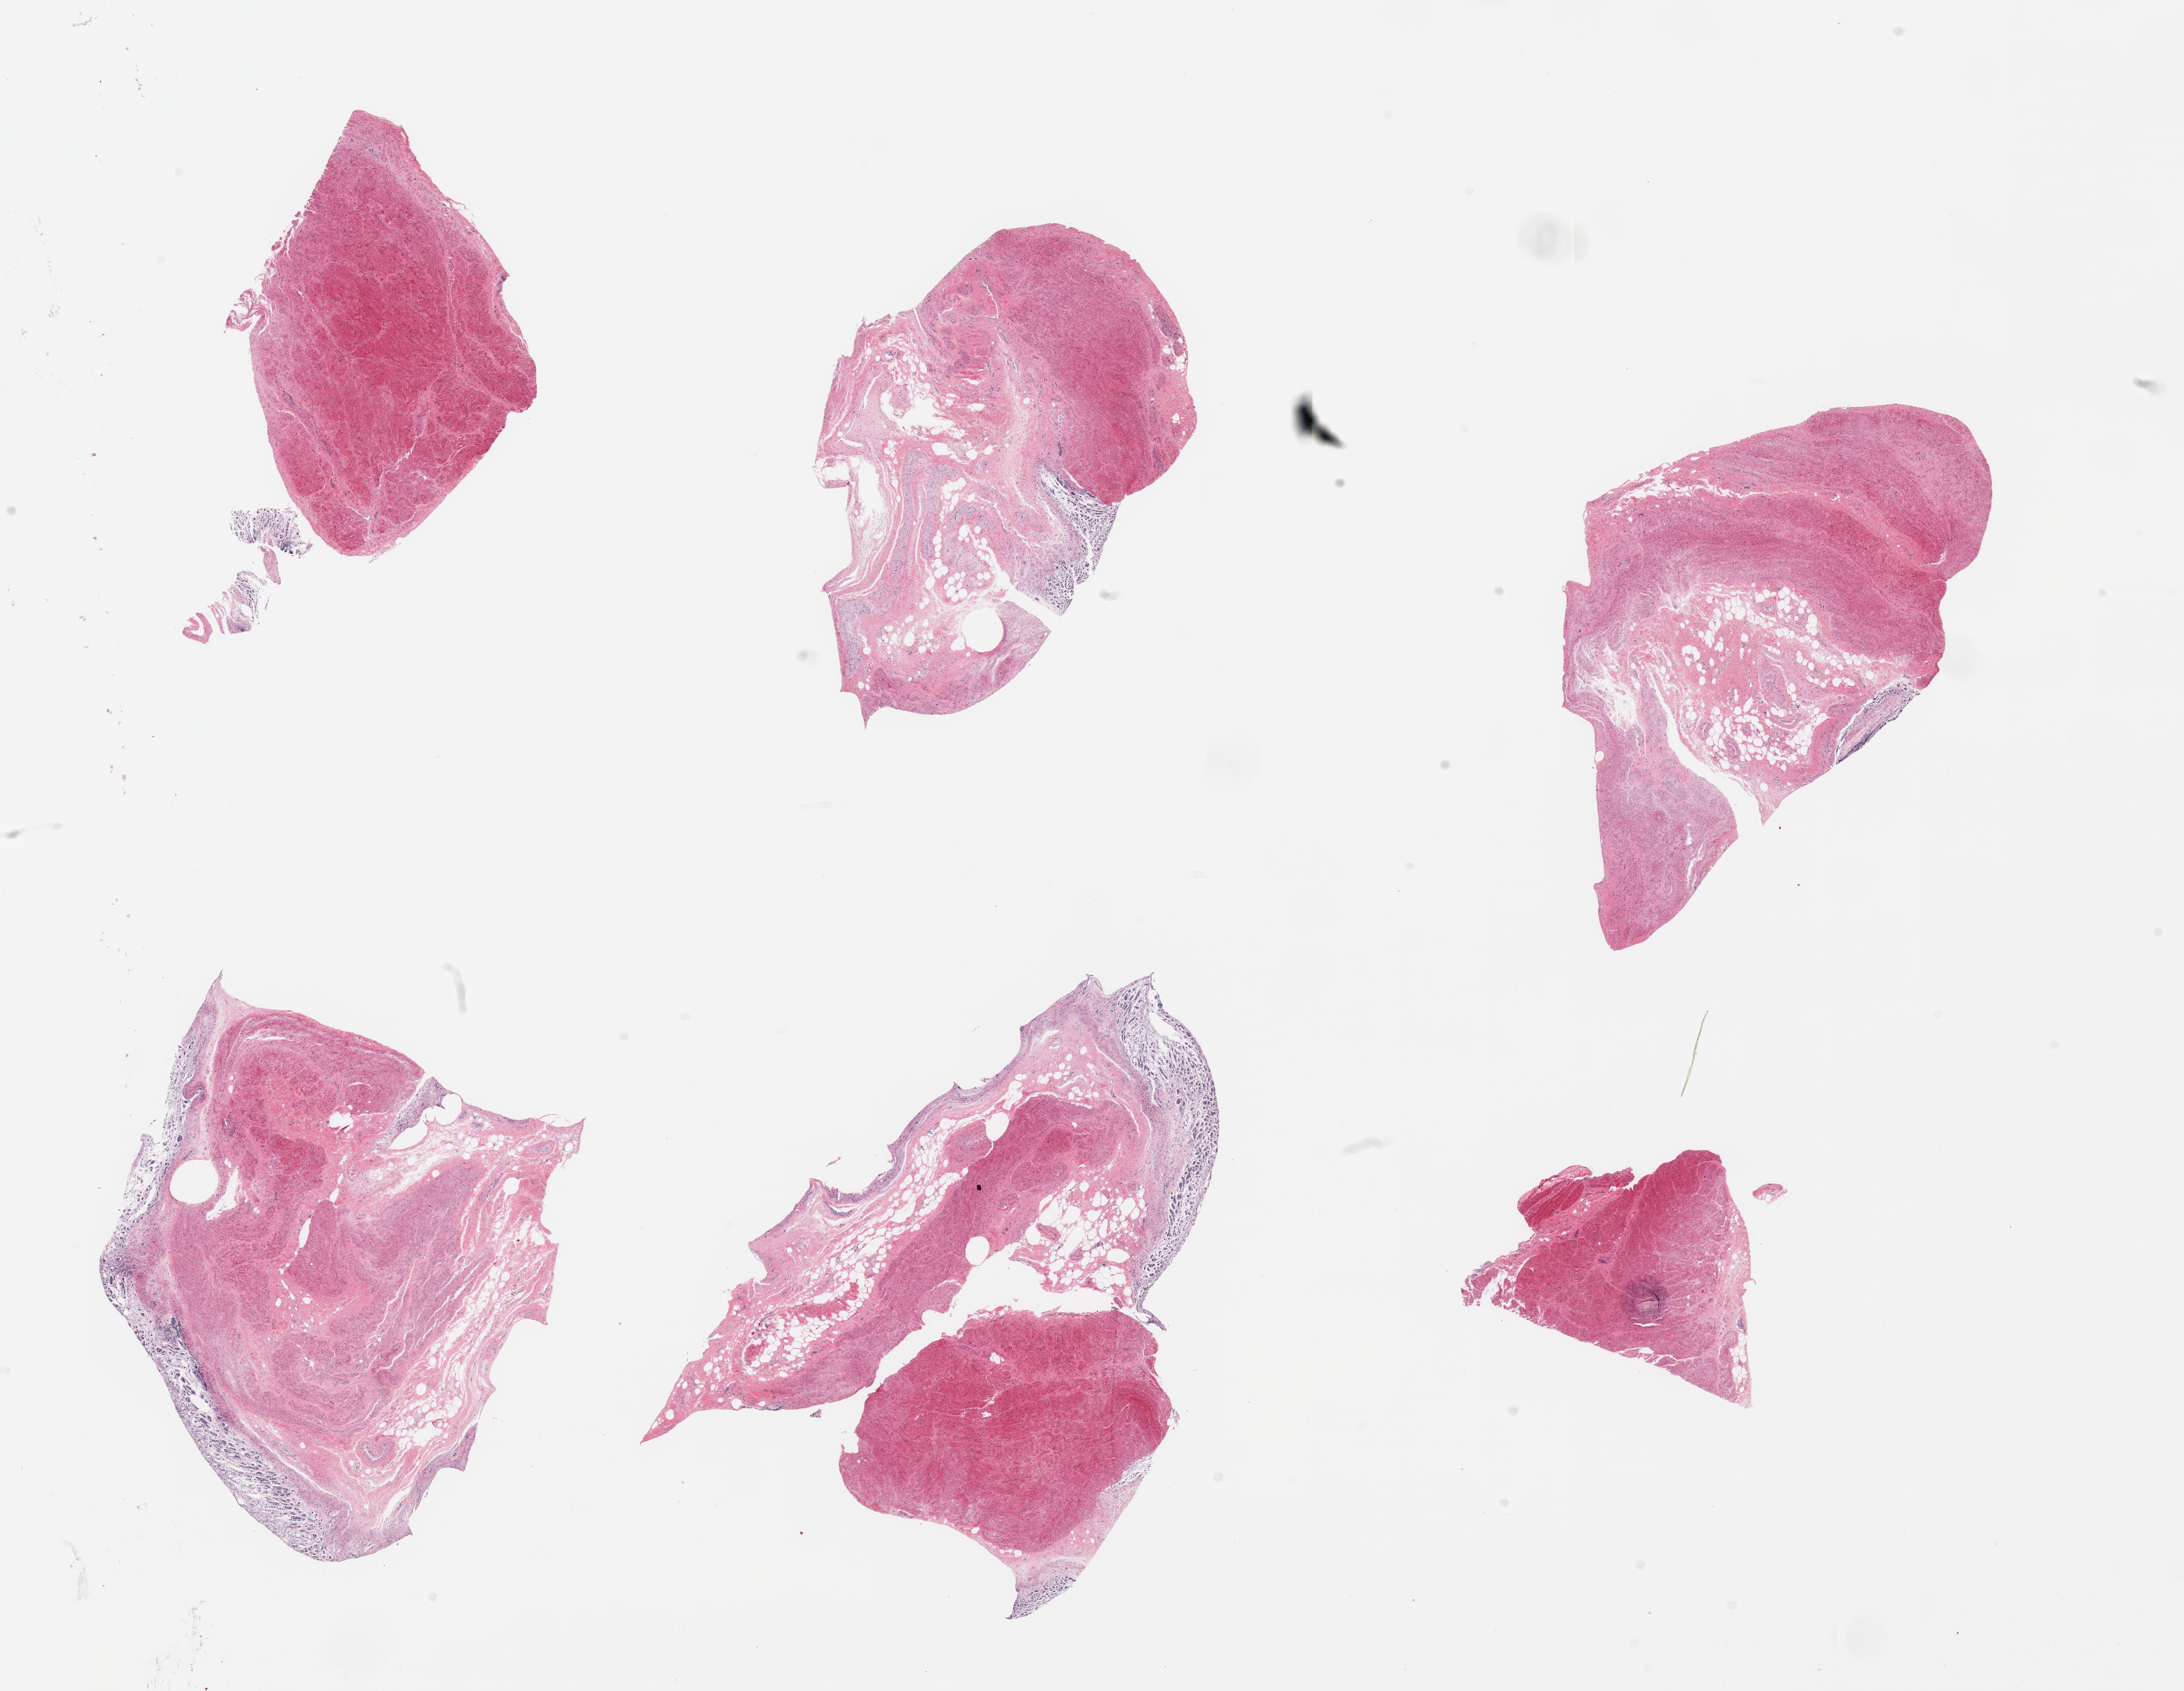
Digitized haematoxylin and eosin-stained section, brightfield, shown as a low-resolution overview of the whole scanned area (about 24.6 x 19.1 mm, slide scanned at 20x); PAXgene-fixed paraffin-embedded (PFPE) section; target tissue: gastroesophageal junction; tissue donor sample. Donor sex: male.
Reviewer comment on this tissue sample: 6 pieces; autolyzed muscularis and significant residual autolyzed gastric mucosa on several pieces).